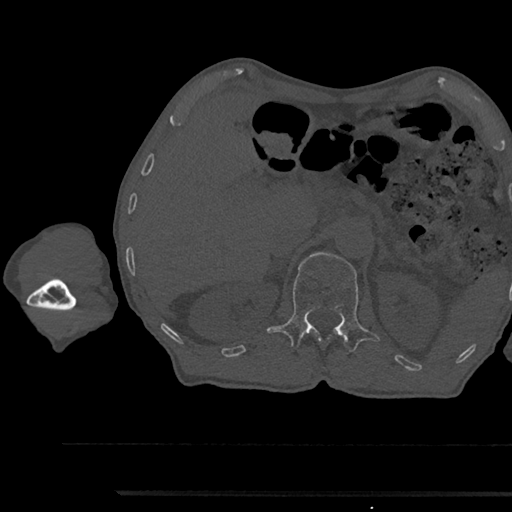
CT including the spine, one axial slice. Slice 657 of 797 in the series (ordered by position). 120 kVp. Bone window (W 1800 / L 400 HU). 0.5 mm slice thickness. 512 × 512 image matrix. Male patient, age 79 years. From the clinical record (not read from this slice): primary cancer: prostate.
Outlined on this slice (semi-automatically segmented with operator editing):
- L1 vertebra: bounding box (x1, y1, x2, y2) in pixels: (267, 252, 380, 351)